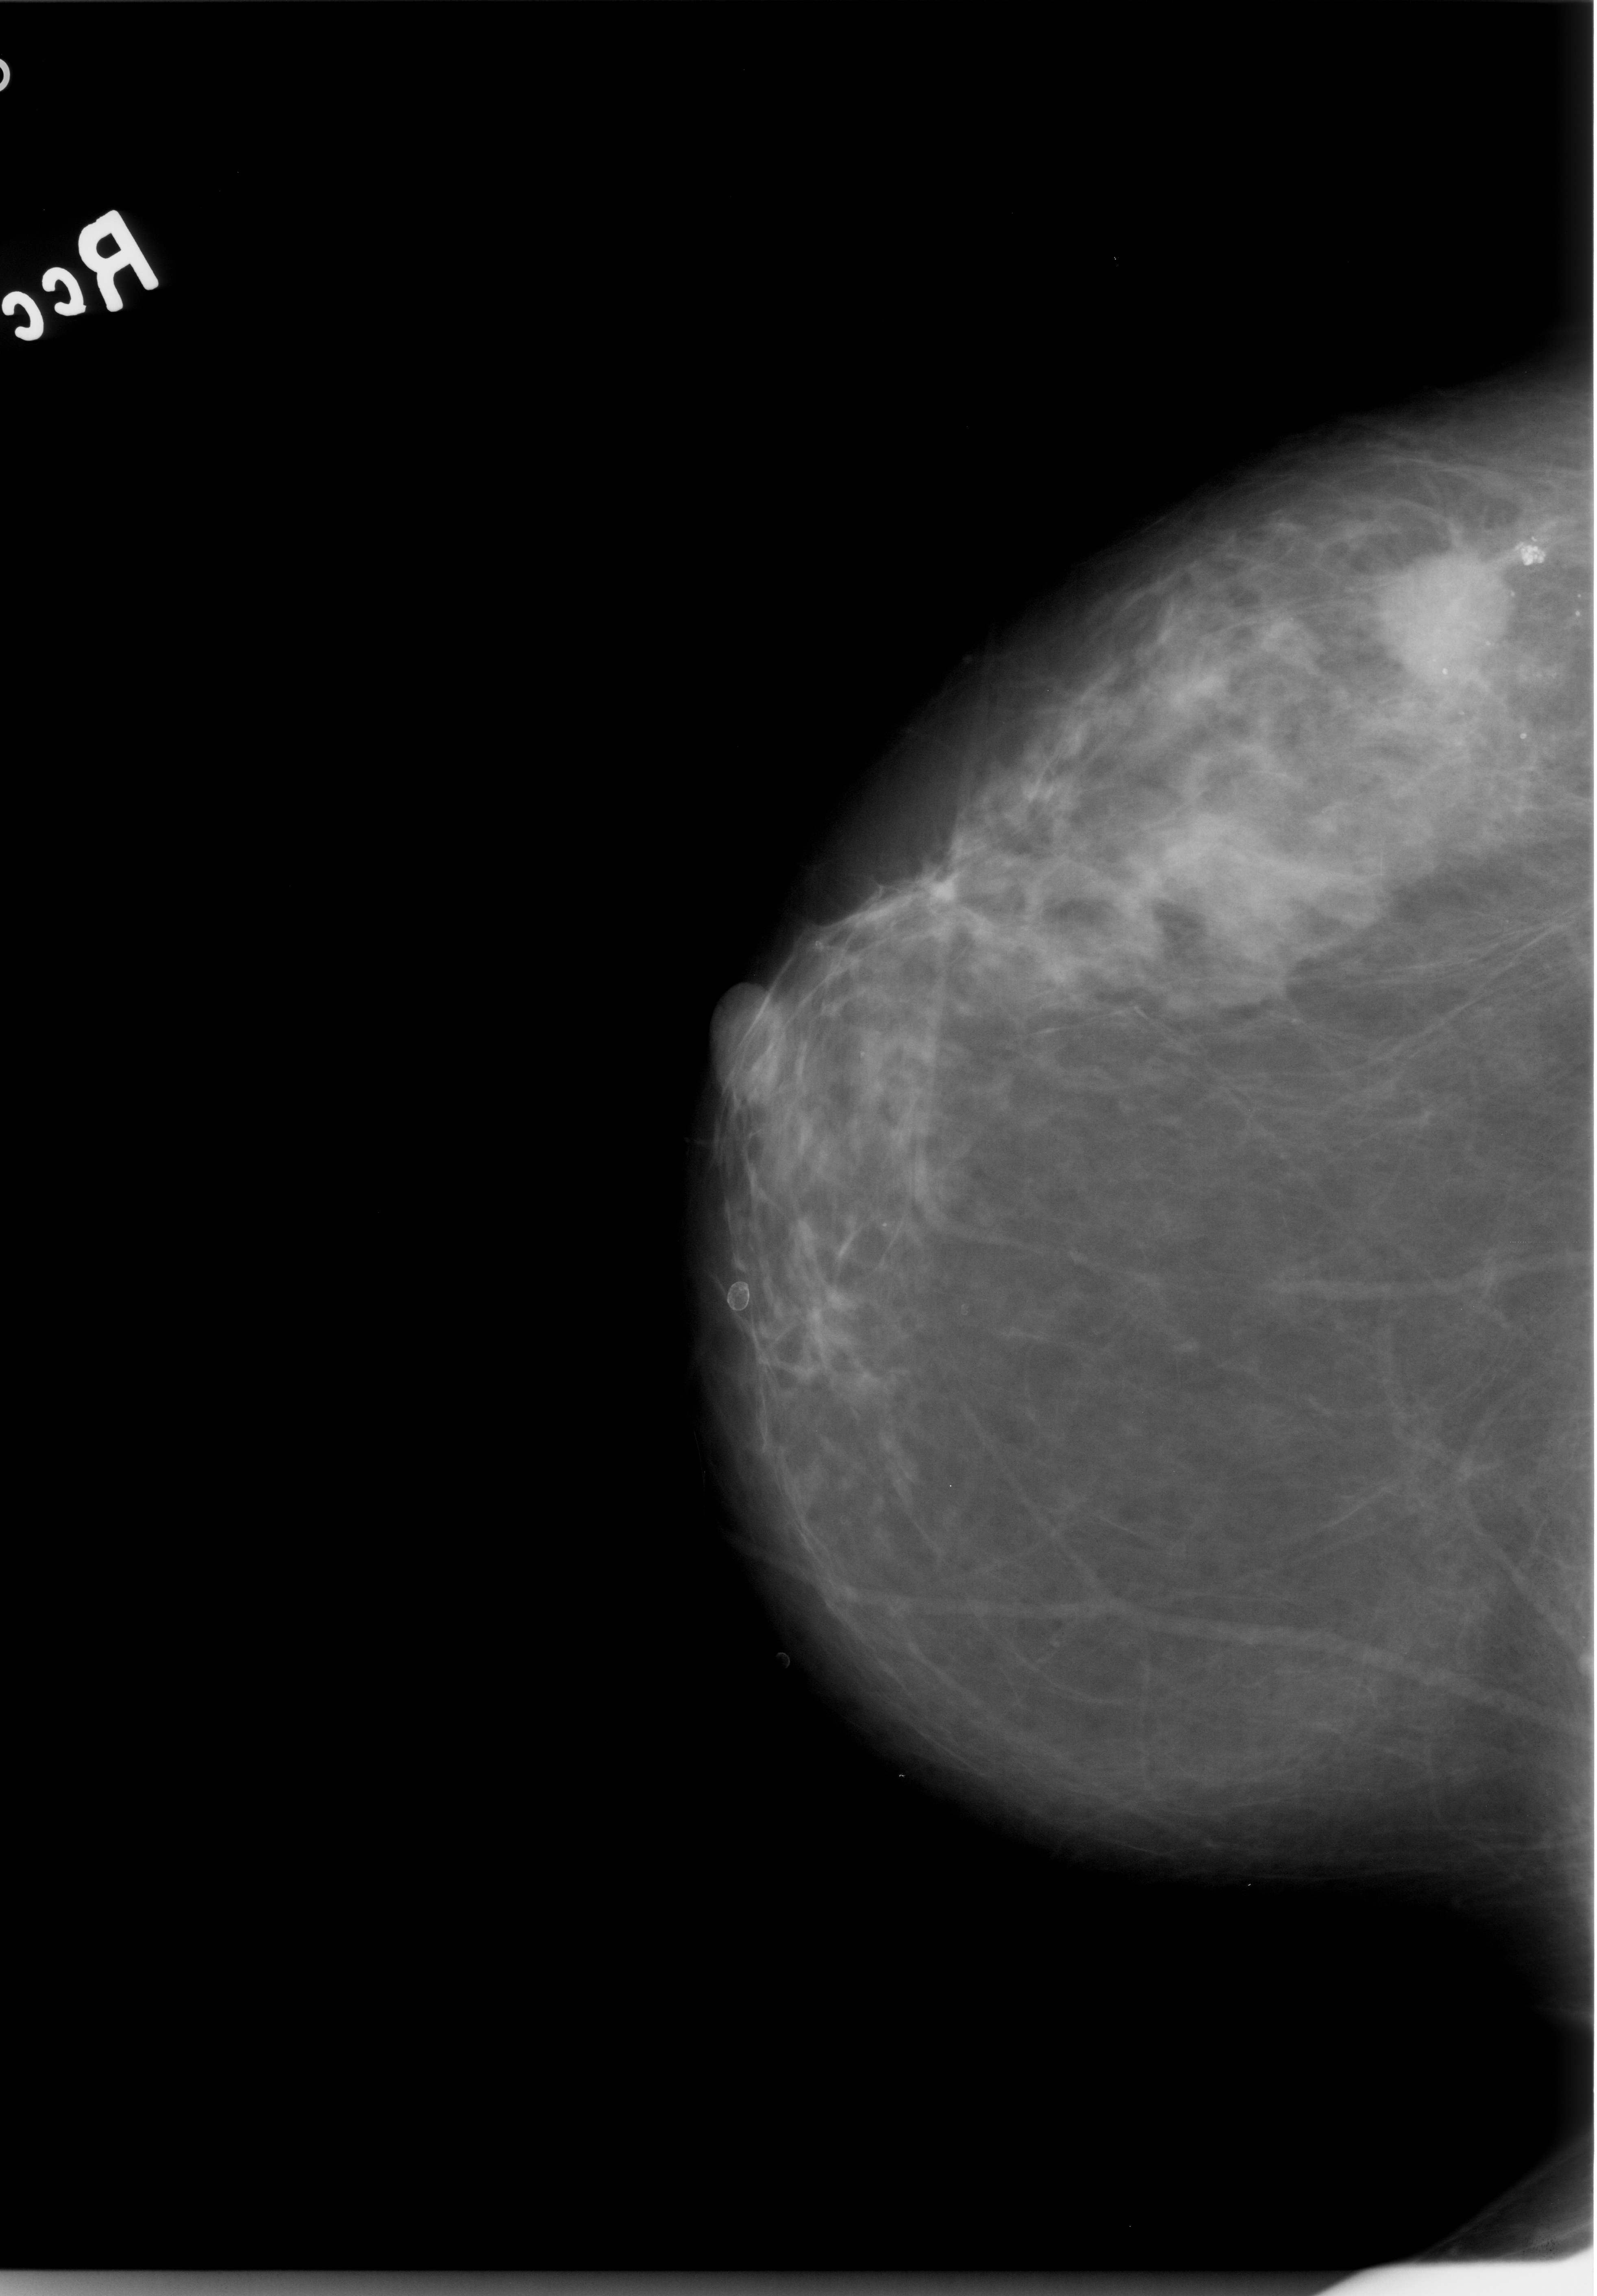
Digitized screen-film mammogram, right breast, craniocaudal (CC) view, BI-RADS breast density category 2 (scale 1–4).
Finding: mass, shape irregular, margins spiculated; BI-RADS assessment category 4; pathology (as recorded): malignant.